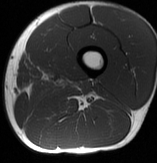
MRI of an extremity soft-tissue mass, one axial slice. Slice 16 of 70 in the series (ordered by position). MR volume resampled by the dataset authors to the PET/CT grid (not the native acquisition matrix). 3.27 mm slice thickness. 157 × 163 image matrix, field of view 153 × 159 mm. Male patient. Case-level facts recorded for this patient, not image findings: histological type: extraskeletal osteosarcoma; grade: high; site of the primary tumour: left adductur.
Outlined on this slice (expert contour drawn on MRI and transferred to this co-registered scan by the dataset authors):
- gross tumour volume (mass): bounding box [x1, y1, x2, y2] px = [74, 81, 91, 93]